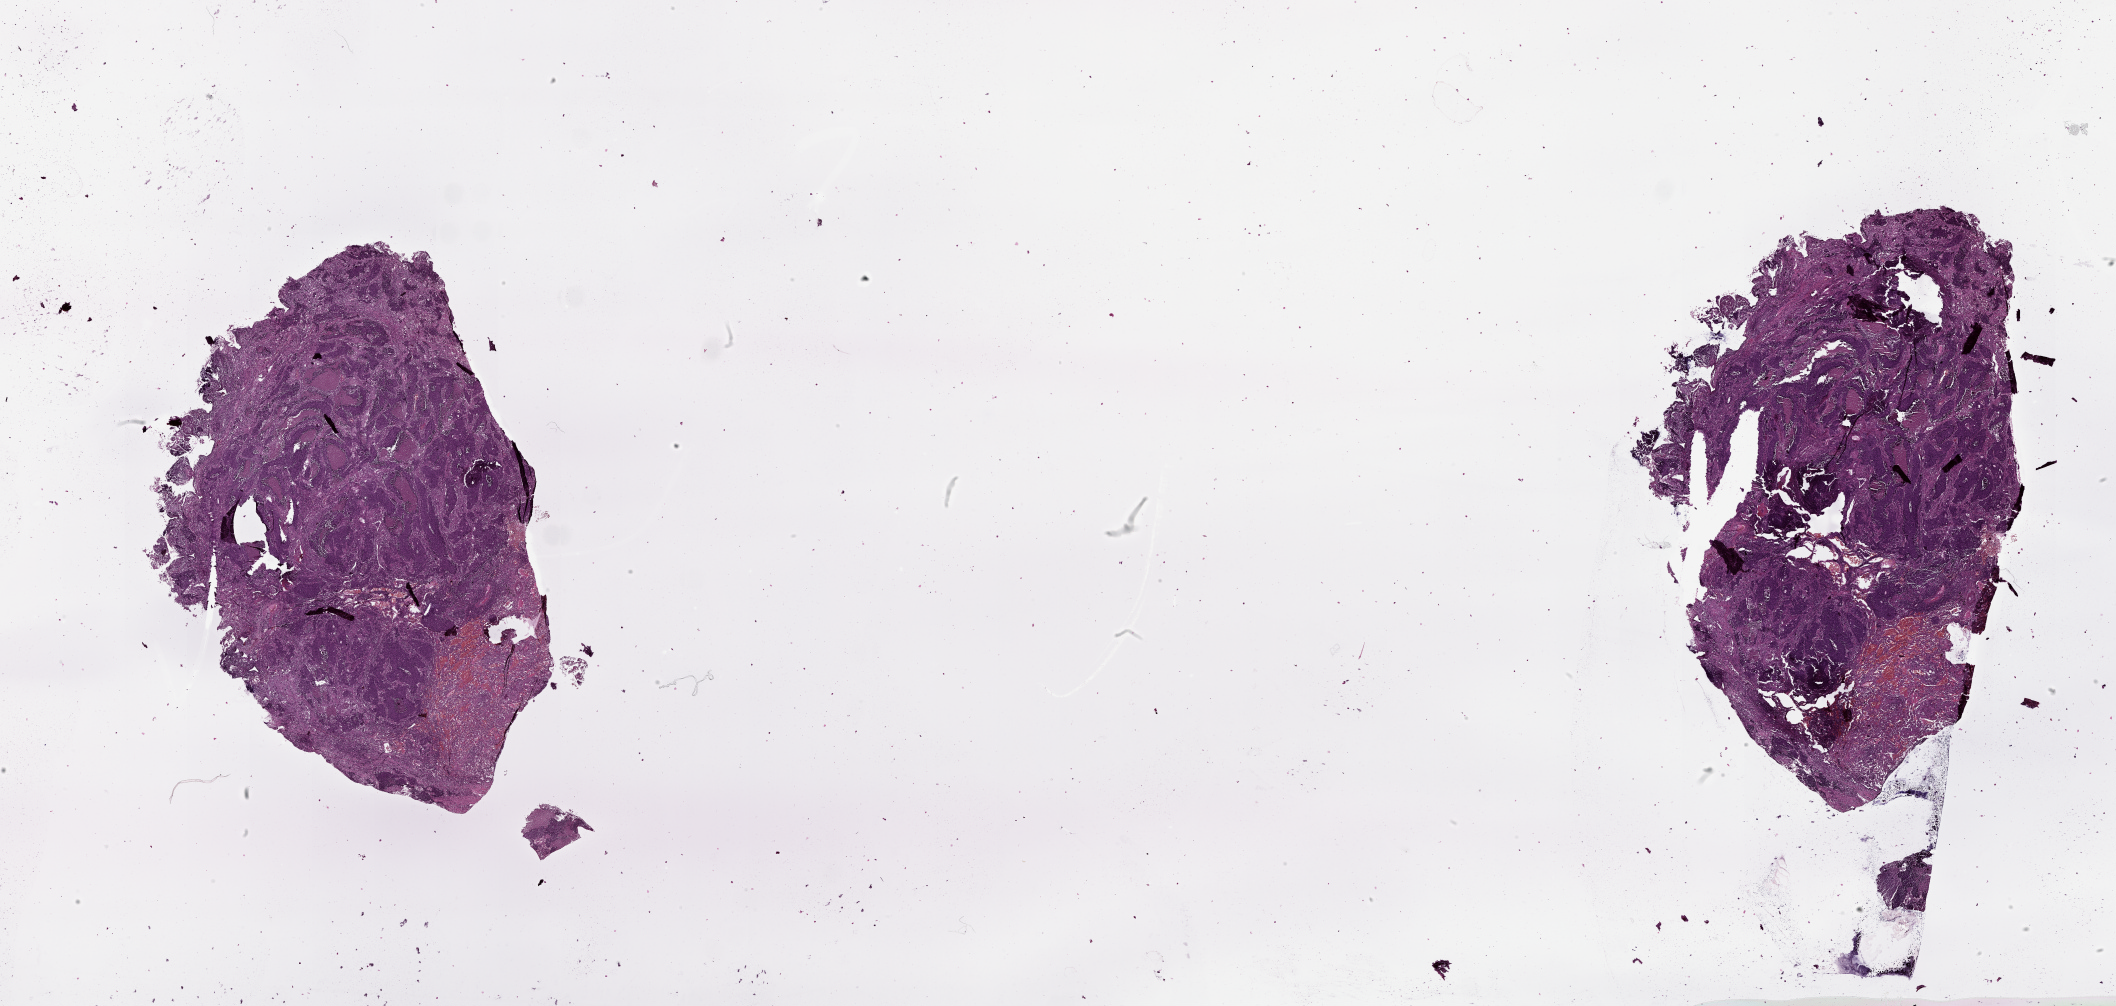
Whole-slide histology image, H&E, shown as a low-resolution overview of the whole scanned area (about 34.1 x 16.2 mm, acquisition: 20x scan), lung, tumour tissue. Male, 68 y/o.
• patient diagnosis (cohort enrolment): squamous cell carcinoma (lung)